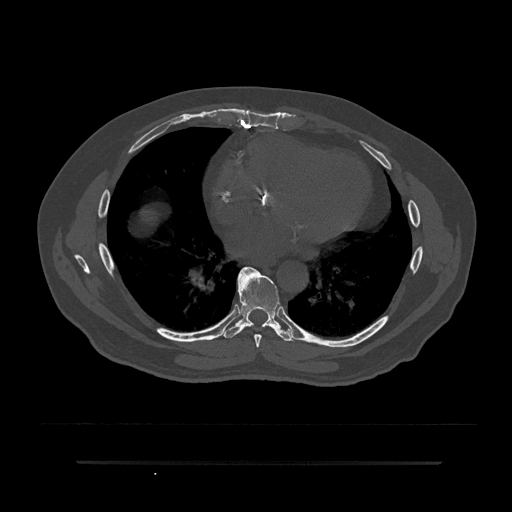
CT including the spine, one axial slice; slice 448 of 797 in the series (ordered by position); reconstruction kernel Br40s/3; bone window (W 1800 / L 400 HU); 512 × 512 image matrix. Patient: male, 59 years. Case-level facts recorded for this patient, not image findings: primary cancer: bile ducts; vertebrae with lytic lesions (as recorded): T10.
Annotated regions visible in this slice (semi-automatically segmented with operator editing):
- T7 vertebra: box from (x=238, y=267) to (x=262, y=348) px
- T8 vertebra: (x=222, y=269)–(x=295, y=342)